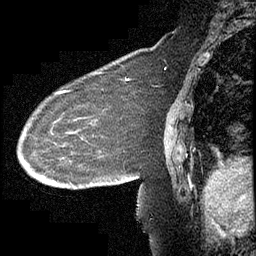
Breast MRI (dynamic contrast-enhanced), one sagittal slice; slice 148 of 232 in the series (ordered by position); dynamic contrast-enhanced study with each time point stored as its own series, time point 2 of 4 at this slice position (early post-contrast, ordered by acquisition time); 1.5 T; TE 4.2 ms, TR 6.7 ms; 3 mm slice thickness; 256 × 256 image matrix. Patient: female, 63 years. Case-level facts recorded for this patient, not image findings: setting: breast cancer imaged before/during neoadjuvant chemotherapy; receptor status: triple-negative.
Annotated regions visible in this slice (semi-automatically segmented with operator editing):
- analysis volume of interest (the breast-tissue region the enhancement analysis was run in; not a lesion): bounding box <17,90,140,211> (left, top, right, bottom; pixels)
- tumour enhancement mask (voxels above the 70 % enhancement threshold inside the analysis volume of interest): <56,90,117,181>